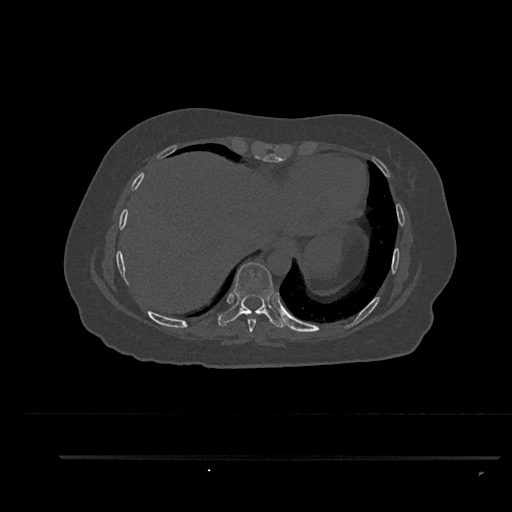
CT including the spine, one axial slice; slice 427 of 797 in the series (ordered by position); reconstruction kernel Br40s/3; 120 kVp; bone window (W 1800 / L 400 HU); 0.5 mm slice thickness; 512 × 512 image matrix, field of view 408 × 408 mm. Patient: female, 44 years. From the clinical record (not read from this slice): primary cancer: renal.
Structures marked on this image (semi-automatically segmented with operator editing):
- T8 vertebra: bounding box <247,311,260,333> (left, top, right, bottom; pixels)
- T9 vertebra: <218,262,285,328>